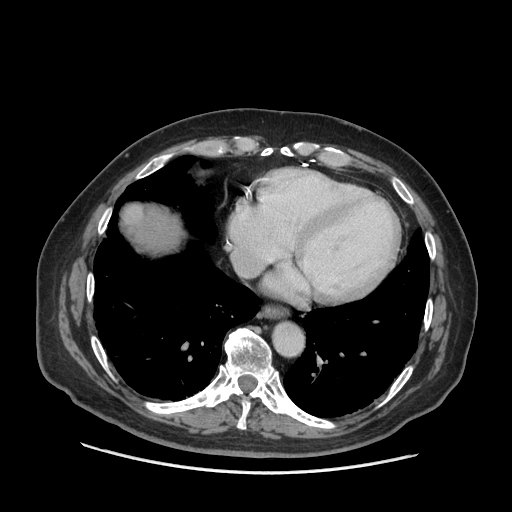
Contrast-enhanced abdominal CT (liver protocol), one axial slice. Slice 67 of 77 in the series (ordered by position). Reconstruction kernel STANDARD. Soft-tissue window (W 400 / L 40 HU). 512 × 512 image matrix. From the clinical record (not read from this slice): diagnosis: hepatocellular carcinoma (patient treated with transarterial chemoembolisation; whether this scan precedes or follows treatment is not stated here); TNM stage (as recorded): Stage-I; Child-Pugh class: A; tumour differentiation: well differentiated; tumour nodularity: uninodular.
Outlined on this slice (semi-automatically segmented with operator editing):
- liver parenchyma outside the tumour (the mass and vessels are separate outlines, so this box may not span the whole liver): bounding box <122,204,180,251> (left, top, right, bottom; pixels)
- mass: <123,205,143,225>